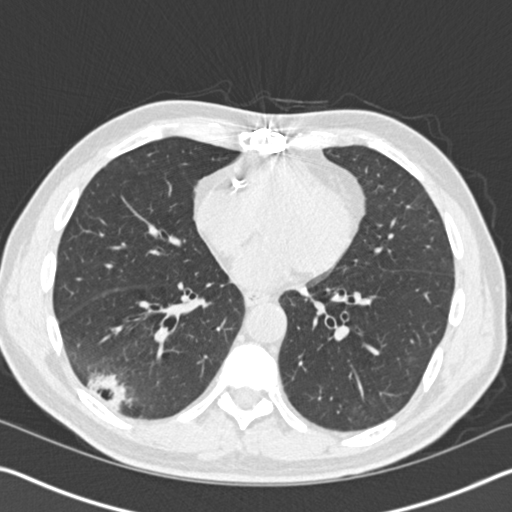
Low-dose screening chest CT, axial slice. Baseline annual screen. Lung window (W 1500 / L -600 HU). 2 mm slice thickness. Standard (soft-tissue) reconstruction kernel (B30f). 512 × 512 image matrix, field of view 340 × 340 mm. Male participant, aged 61 years at enrolment.
- Expert-annotated lung lesion, bounding box <49,328,159,425> (left, top, right, bottom; pixels).
- Reader record for this screening exam (exam-level; its link to the box is not recorded): non-calcified nodule or mass ≥4 mm, right lower lobe, 52 × 36 mm, spiculated (stellate) margins, soft tissue attenuation.
- Official screen result: positive, change unspecified: nodule(s) >= 4 mm or enlarging nodule(s), mass(es), or other non-specific abnormalities suspicious for lung cancer.